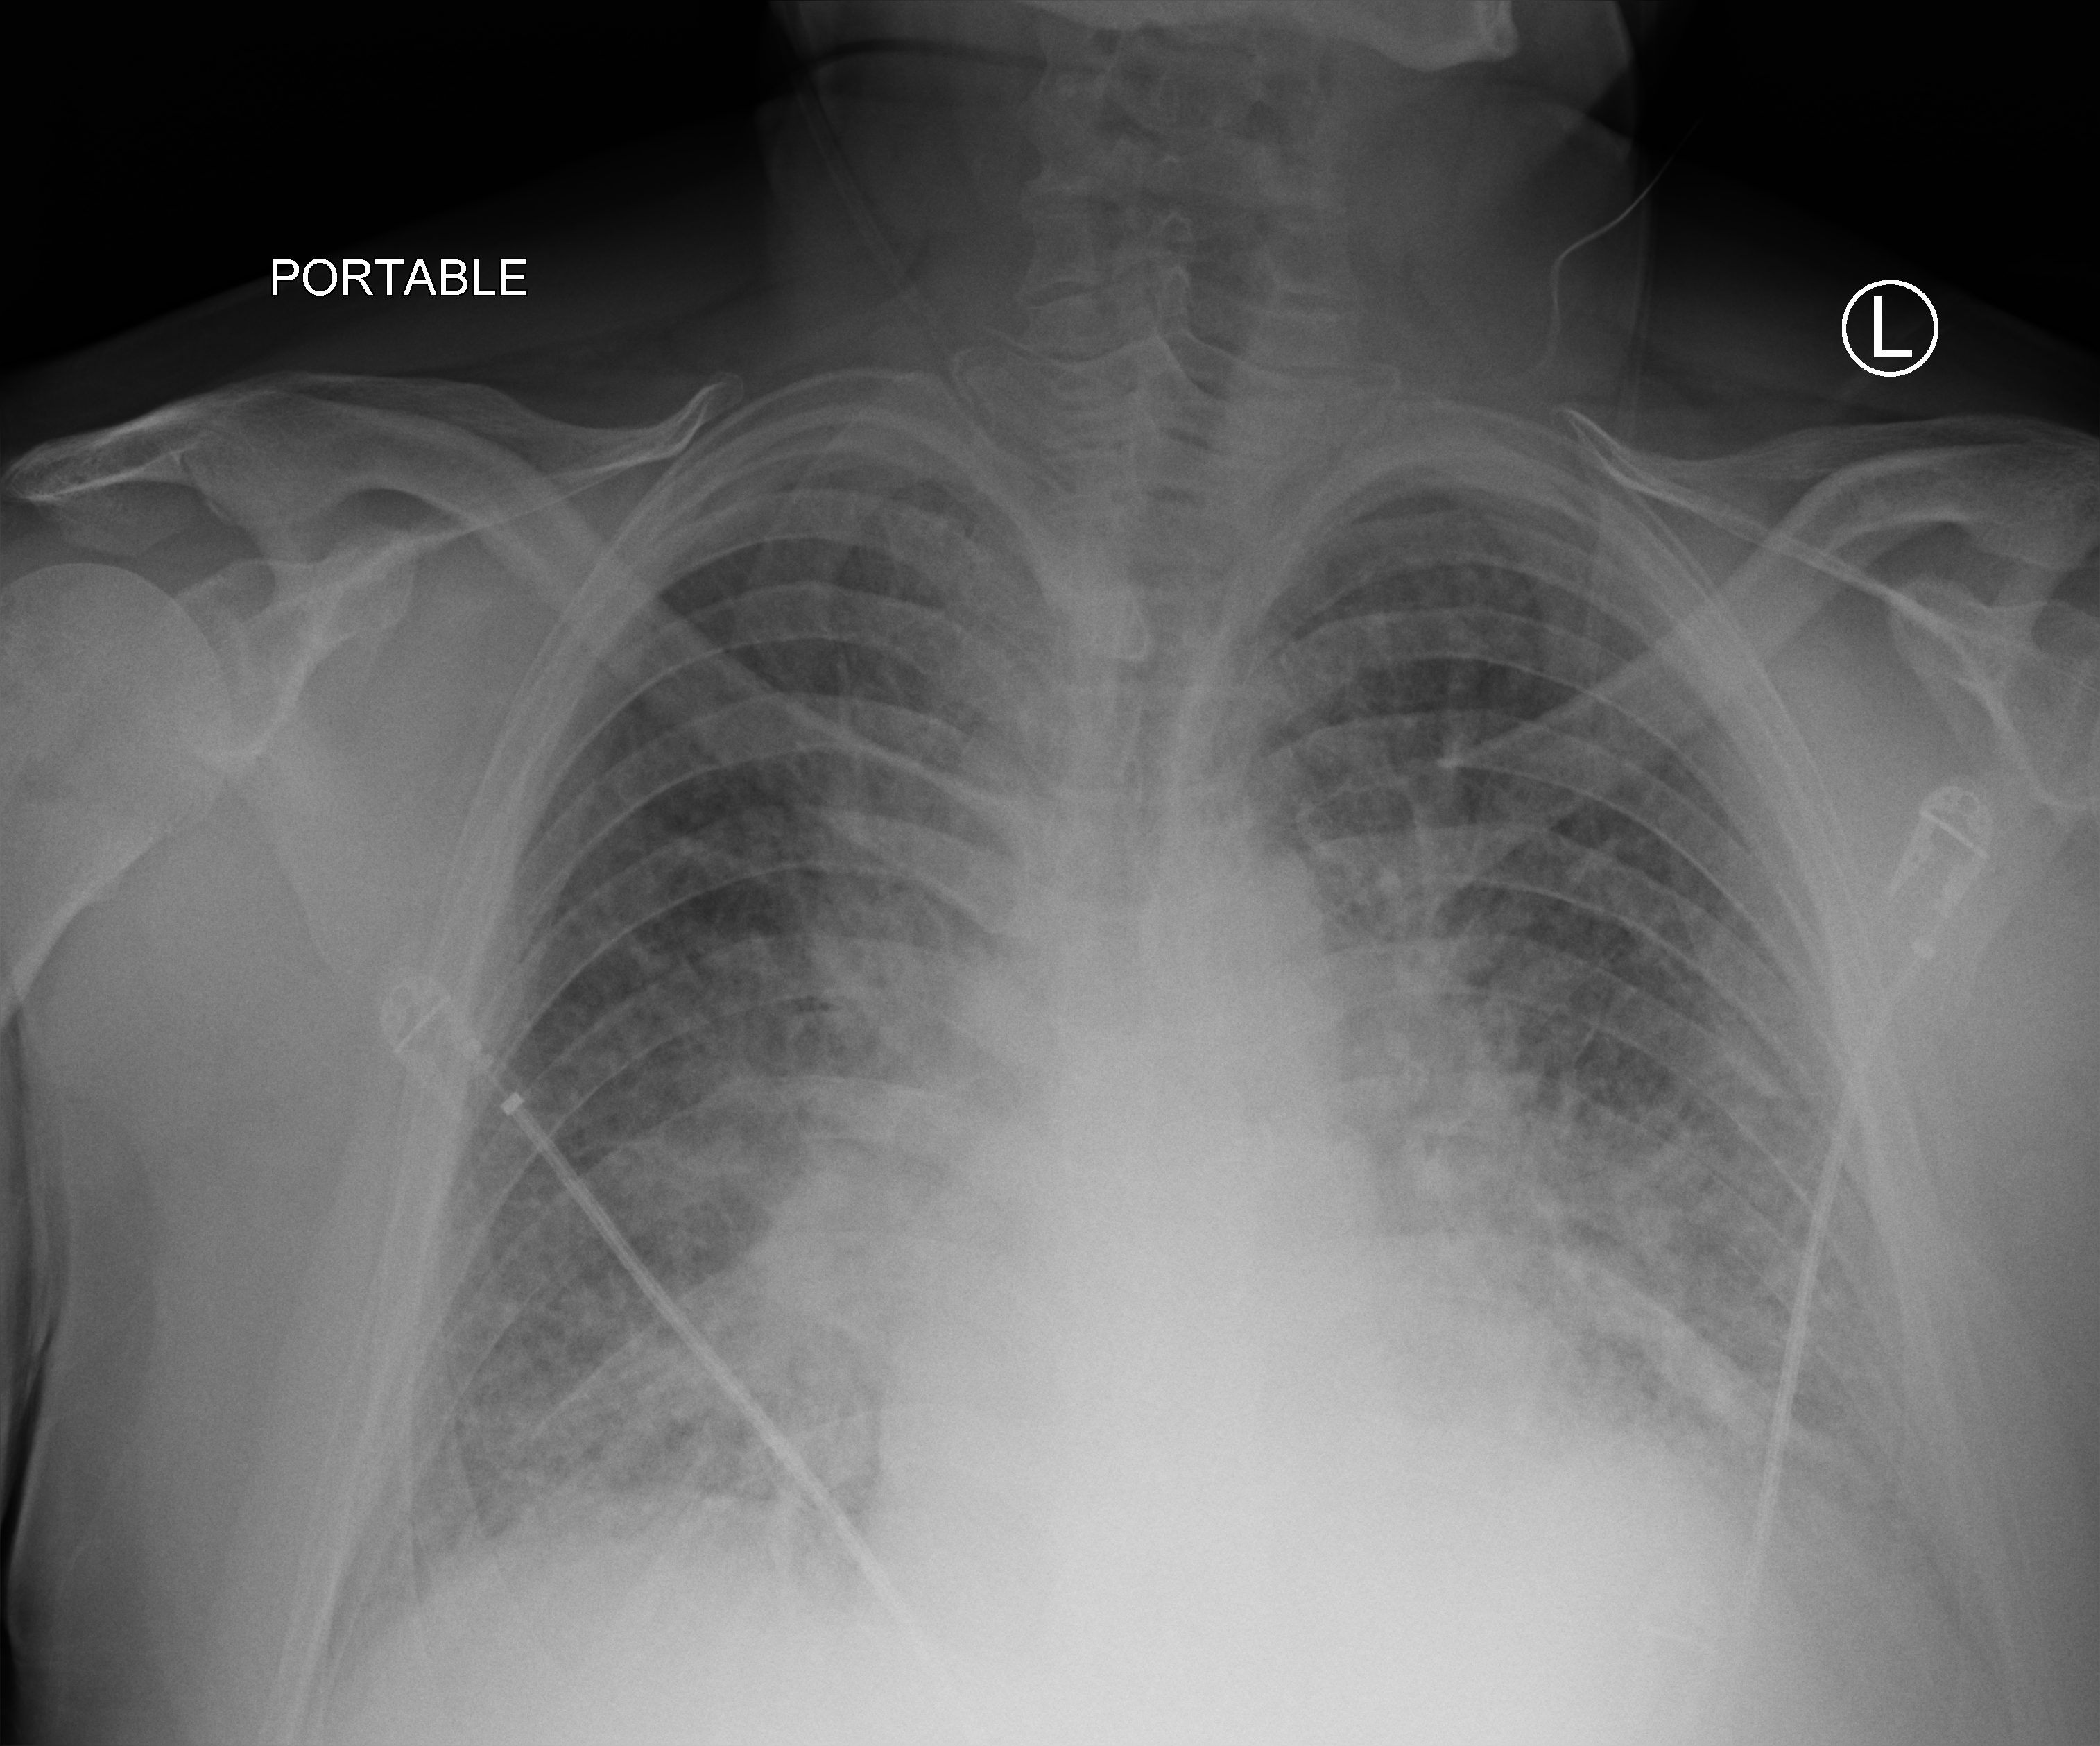
Bedside chest radiograph (computed radiography). Male patient hospitalised with COVID-19, age 18–59 years.
Admission-level facts for this patient (not findings on this image; timing relative to this image not recorded): admitted to intensive care during this hospital stay: no.